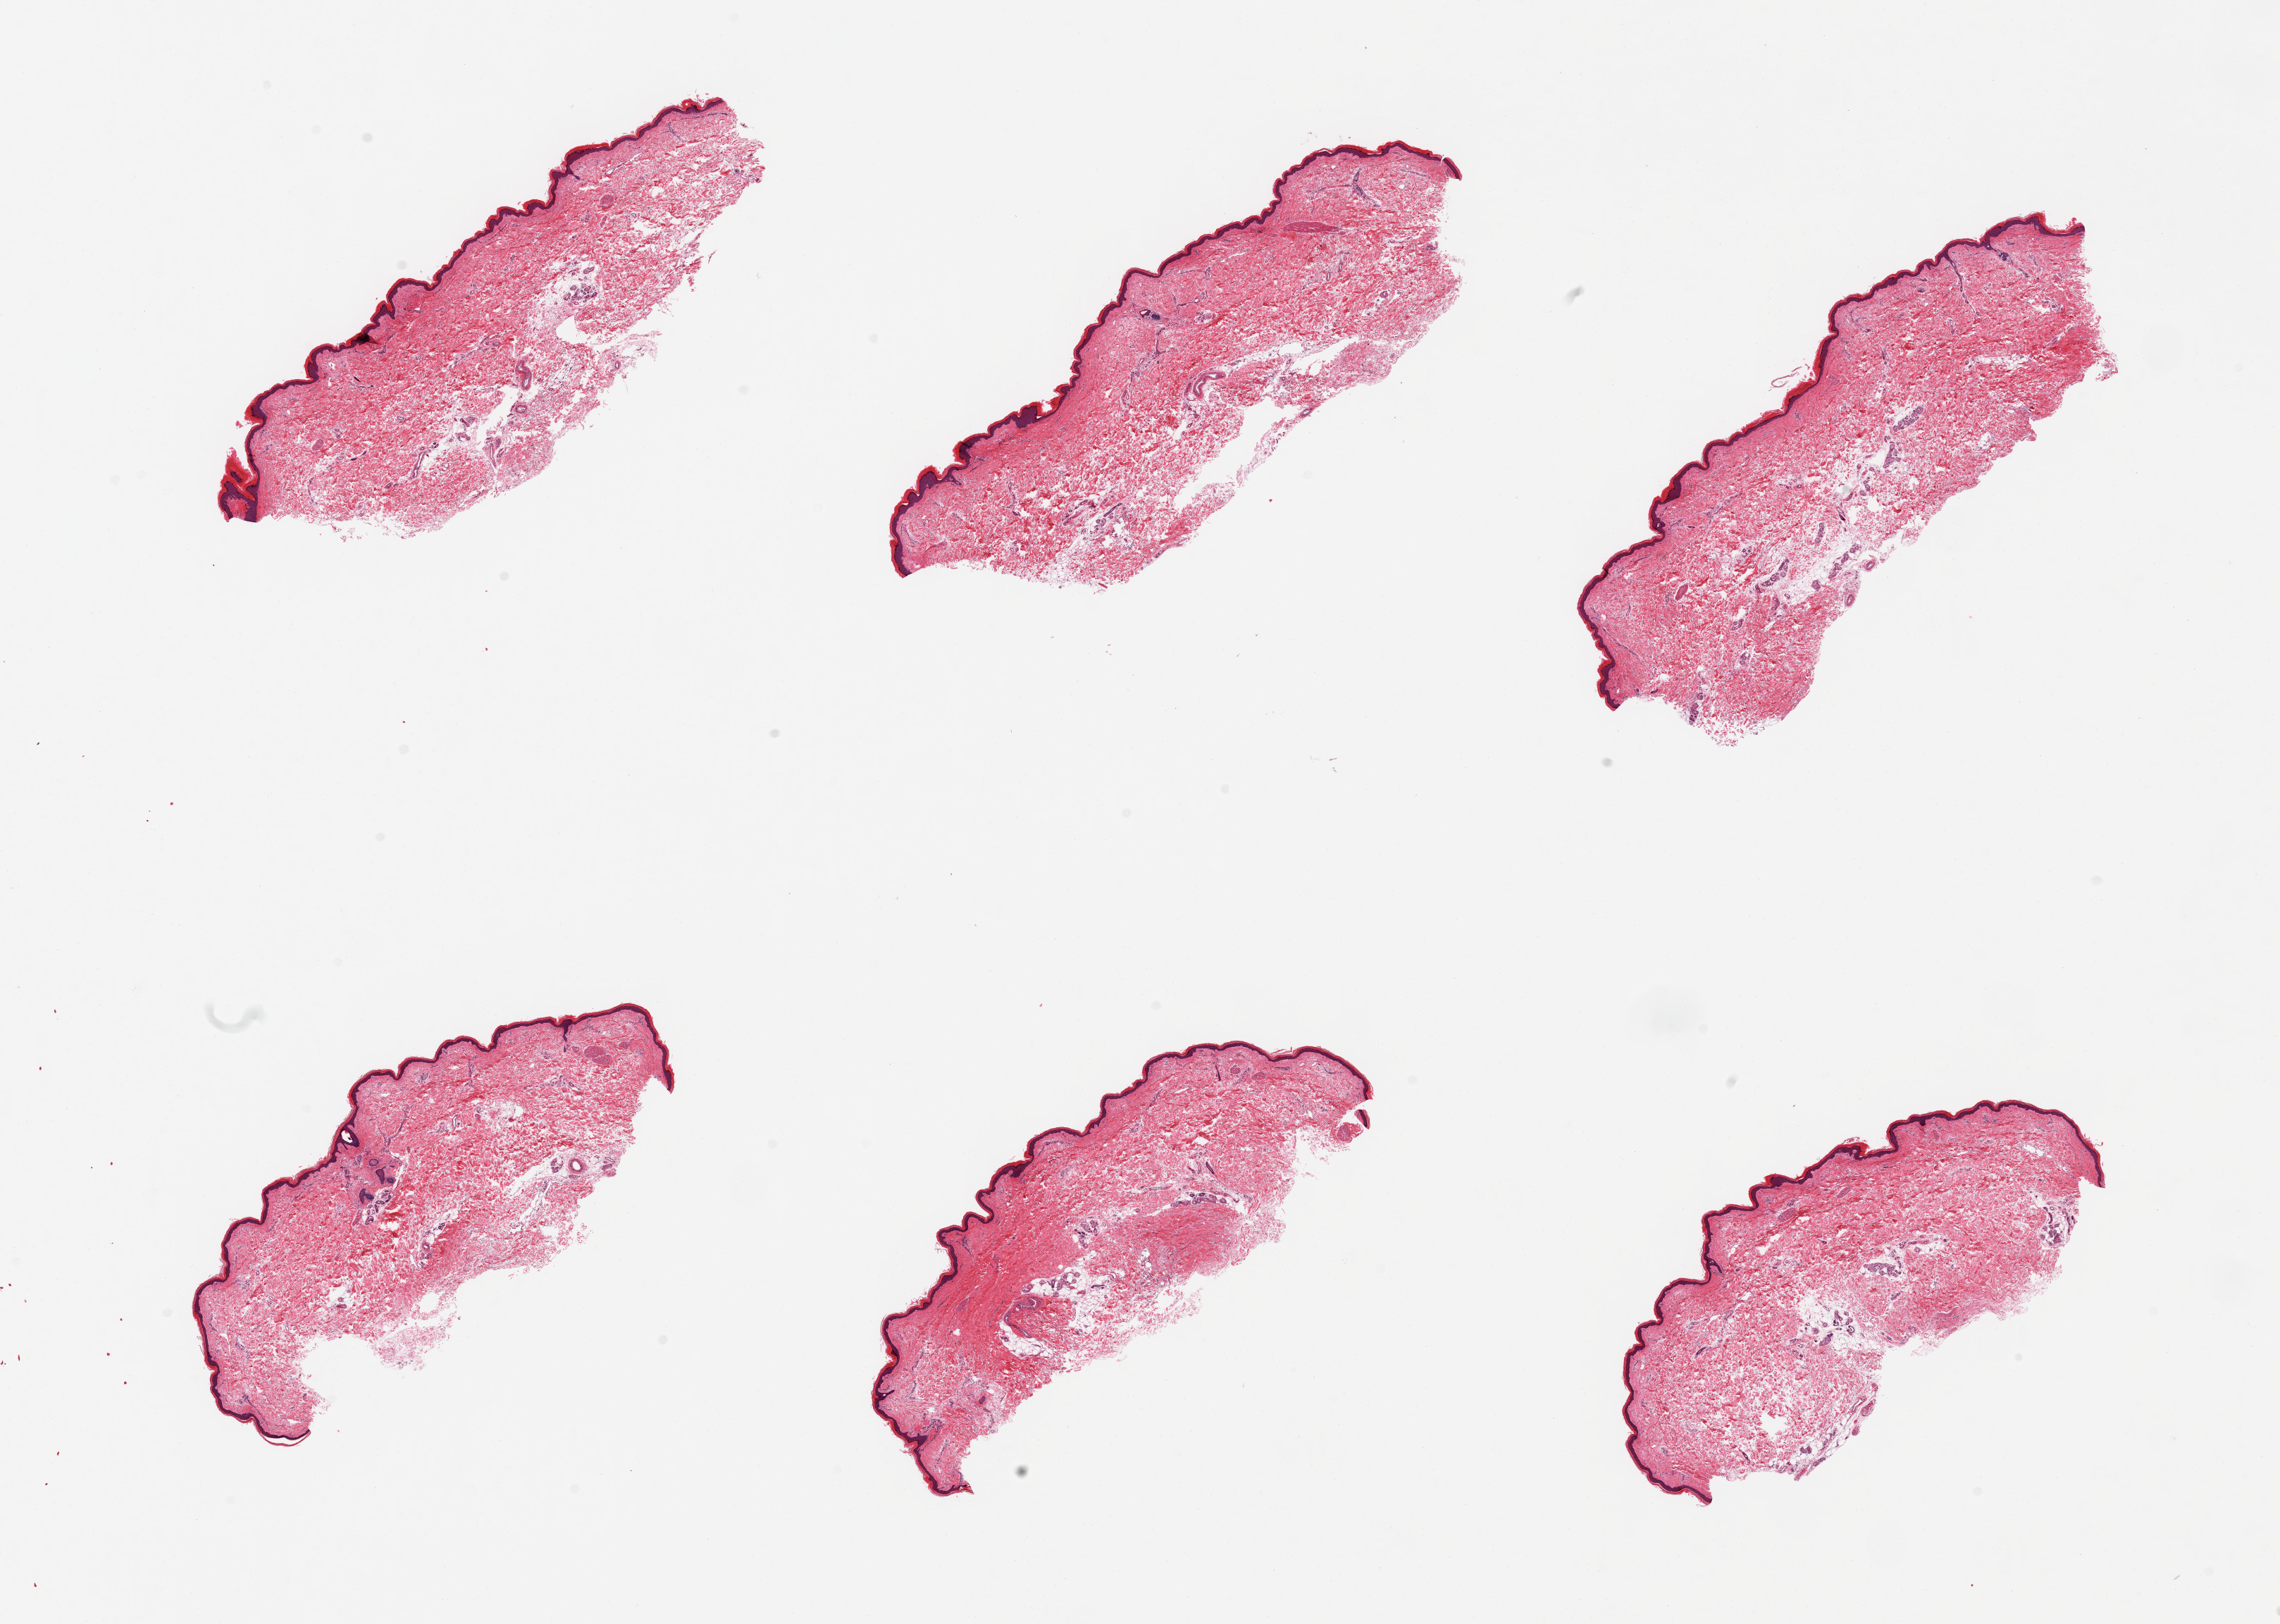
Whole-slide image, H&E stain, a low-resolution overview of the entire scanned area, about 25.6 x 18.2 mm. PAXgene-fixed paraffin-embedded (PFPE) section. Section of skin of lower leg (target tissue). Donor tissue sample. Donor: female.
Pathologist's review note for this sample: 6 pieces, minimal dermal fat; squamous epithelium is ~70 Microns.